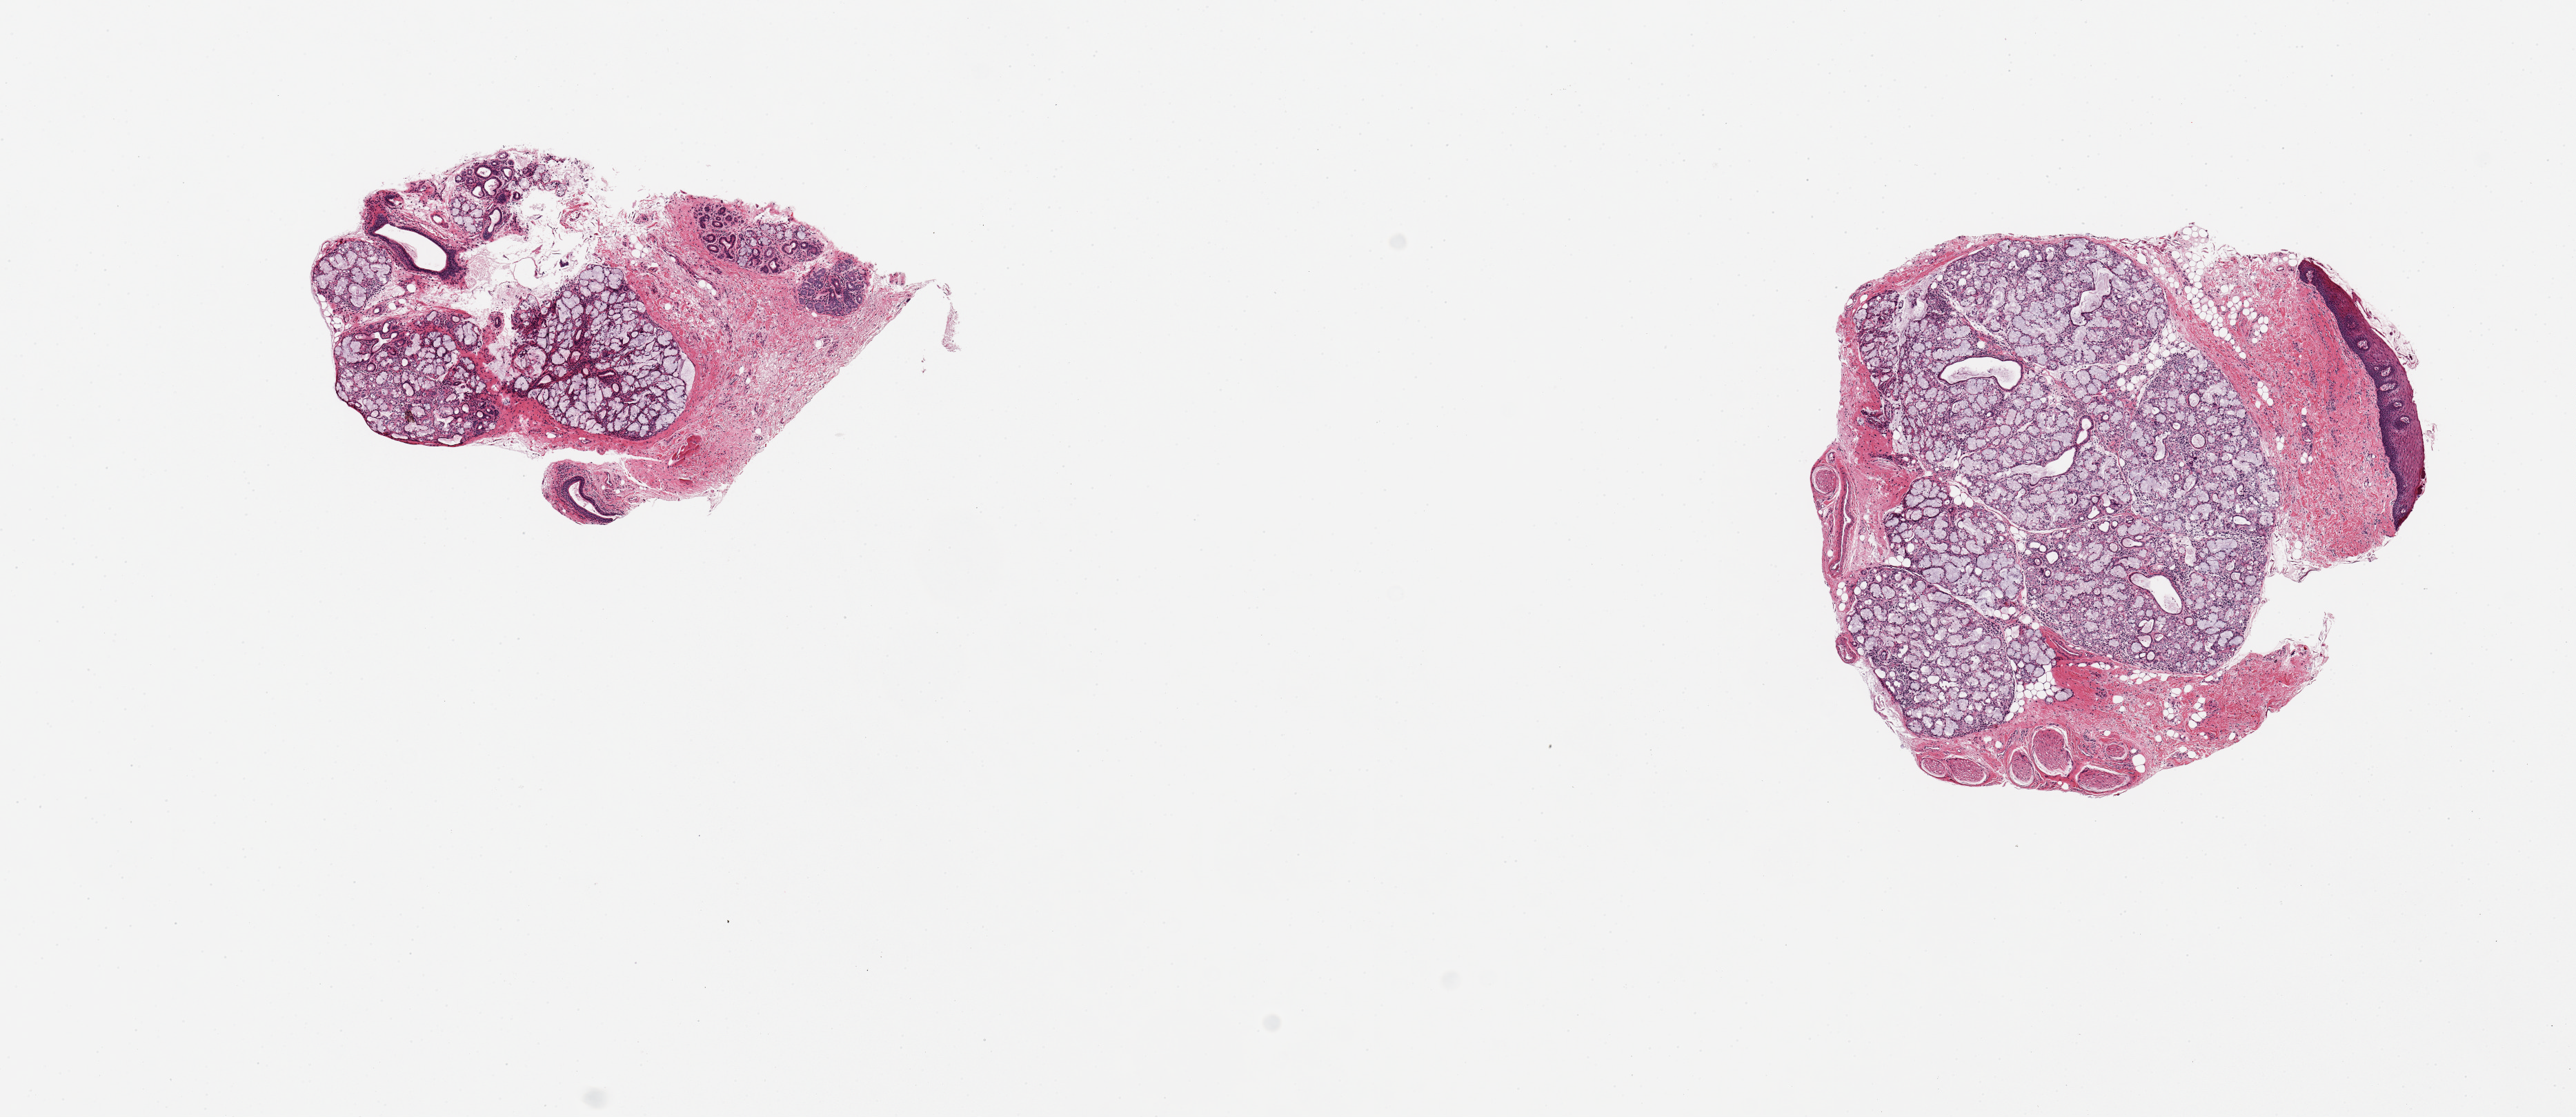
Digitized hematoxylin and eosin (H&E)-stained section, shown as a low-resolution overview of the whole scanned area (about 14.8 x 6.4 mm, slide scanned at 20x); PAXgene-fixed paraffin-embedded (PFPE) section; section of minor salivary gland (target tissue); donor tissue sample. Donor: male.
Pathologist's review note for this sample: 2 pieces glandular elements are ~60-70% of tissue, rest is stroma/squamous mucosa.